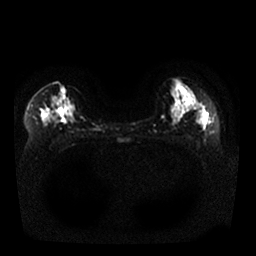
Breast MRI, one axial slice; slice 12 of 25 in the series (ordered by position); diffusion-weighted series; image 2 of 4 stored at this slice position (different b-values; order by instance number); 1.5 T; 4 mm slice thickness; 256 × 256 image matrix. Female patient.
Outlined on this slice (expert manual segmentation):
- tumour on diffusion-weighted imaging: box from (x=41, y=110) to (x=50, y=121) px